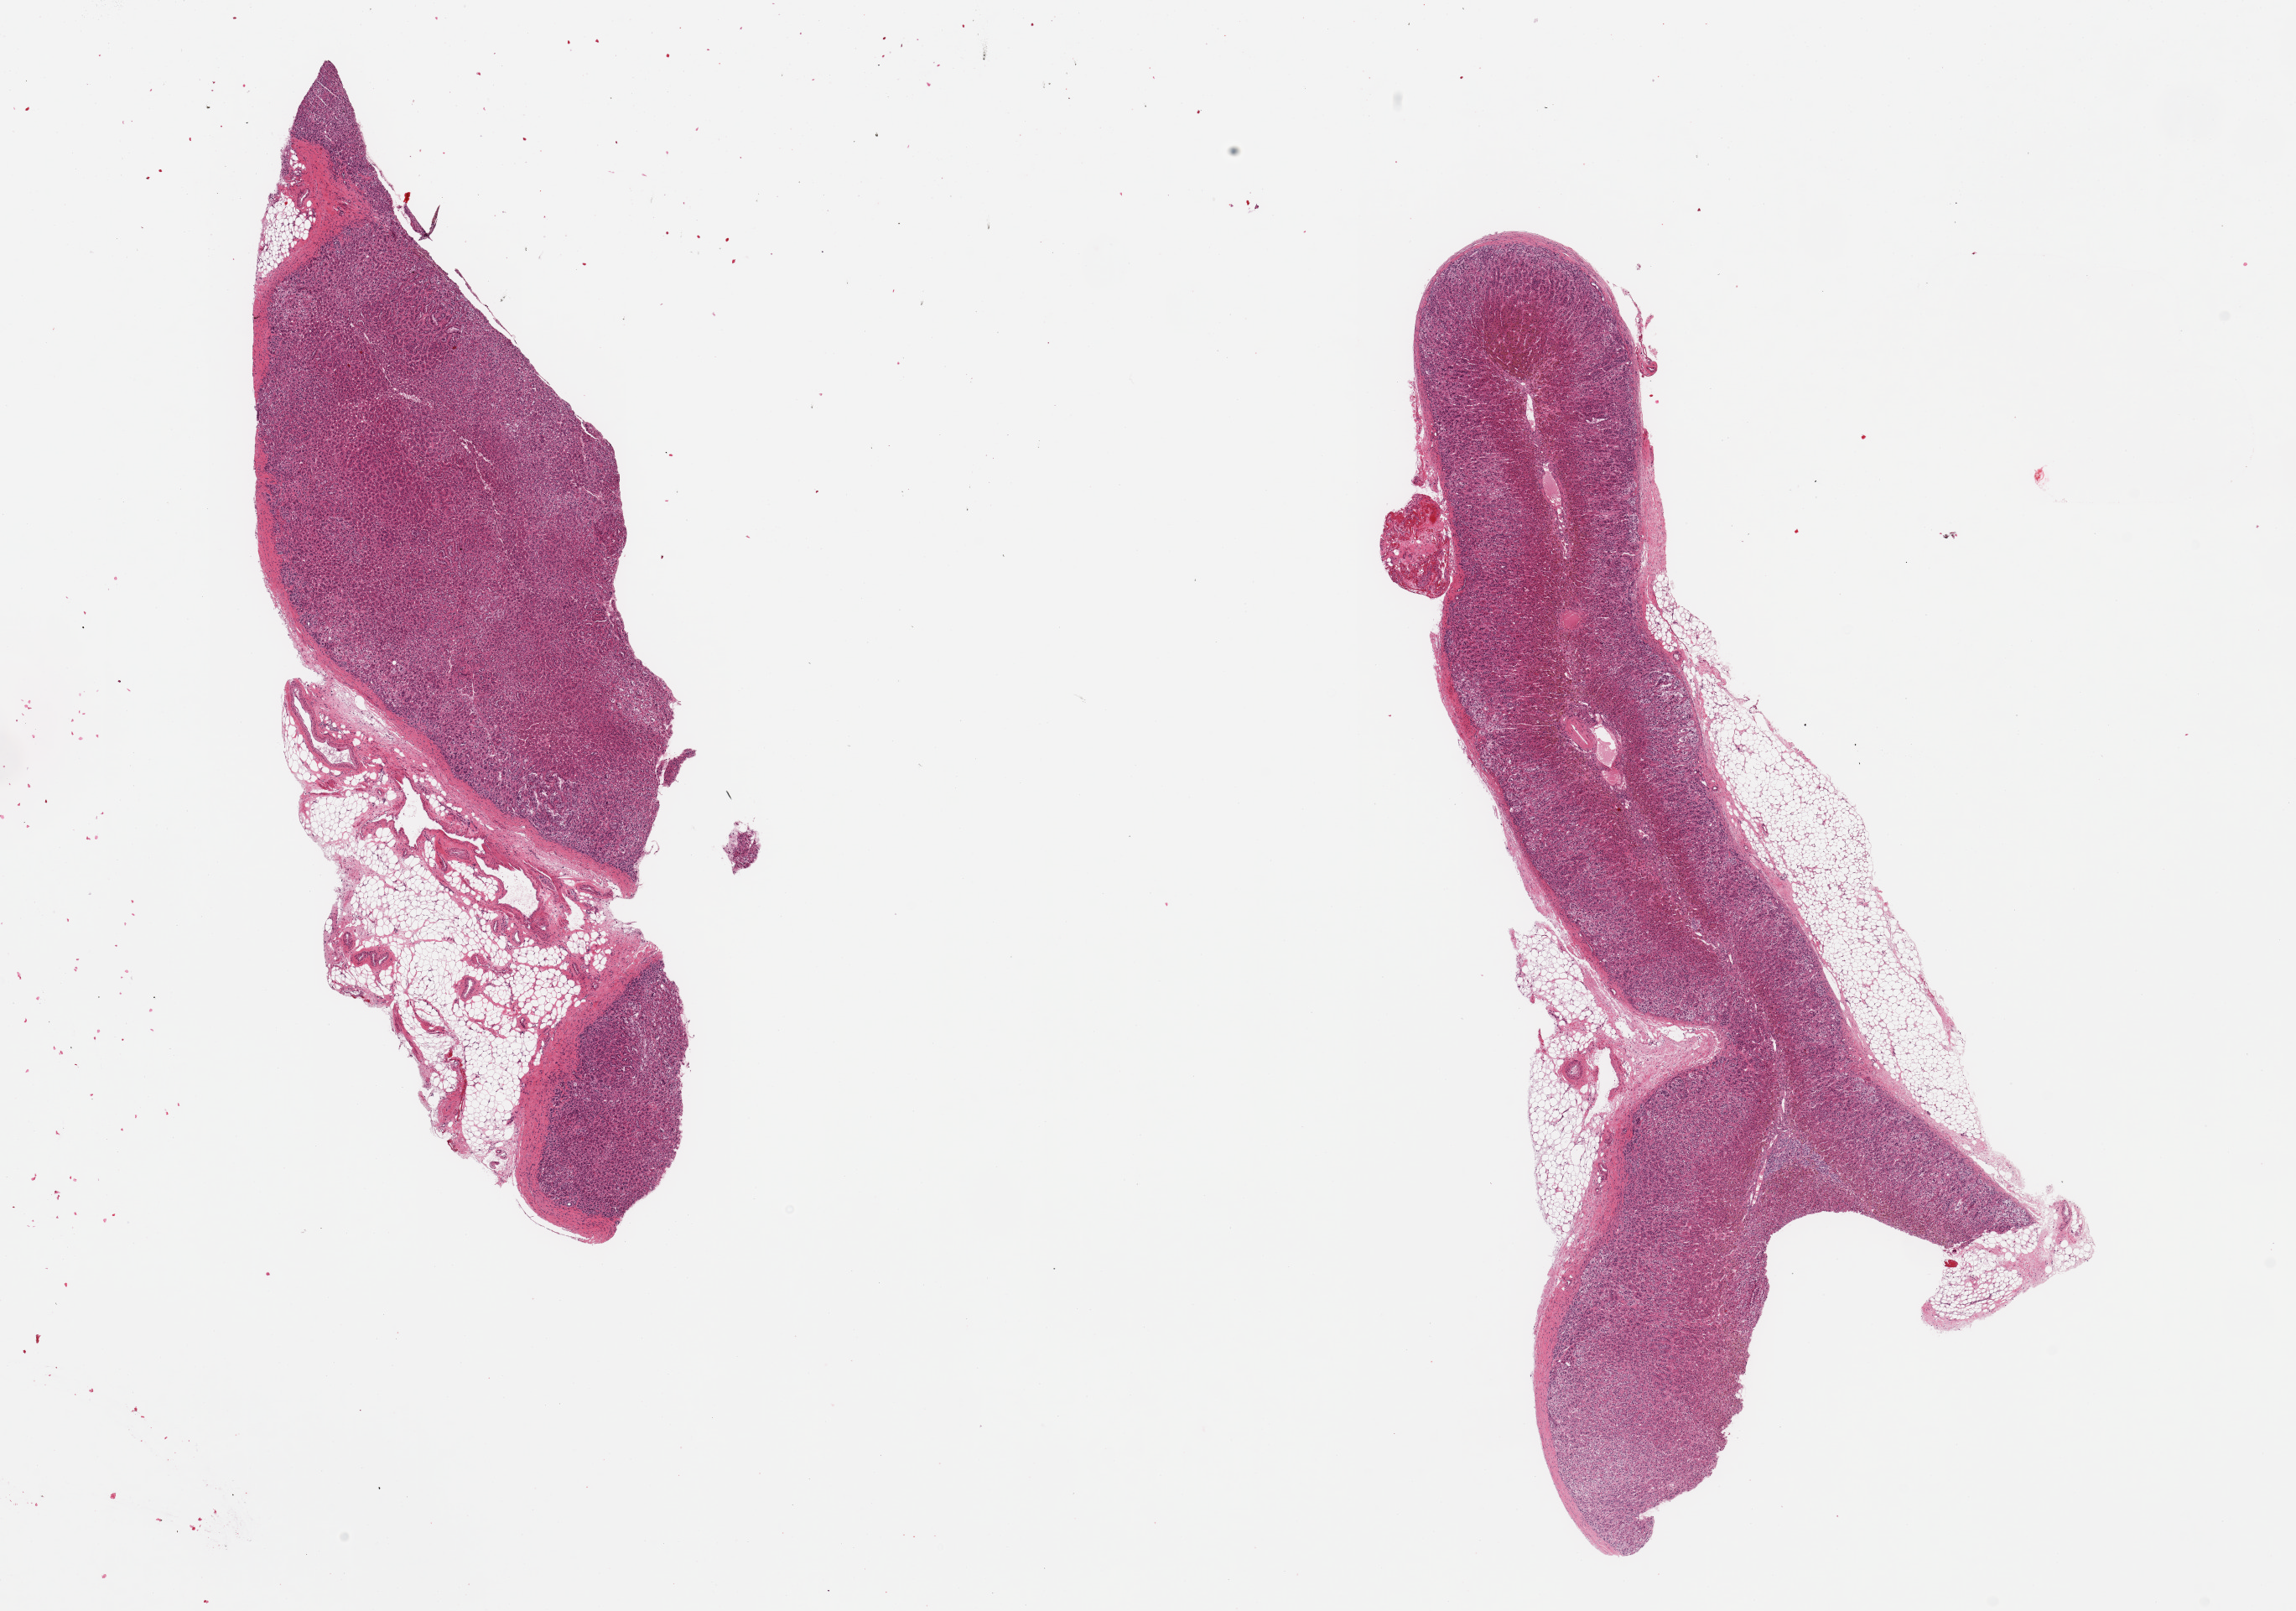
Whole-slide image, hematoxylin and eosin (H&E) stain, whole scanned area (about 21.7 x 15.2 mm, from a 20x scan) shown as a low-resolution overview. PAXgene-fixed paraffin-embedded (PFPE) section. Sampled site (target tissue): adrenal gland. Tissue donor sample. Donor: male.
Review note (as recorded): 2 pieces; 30% external fat.